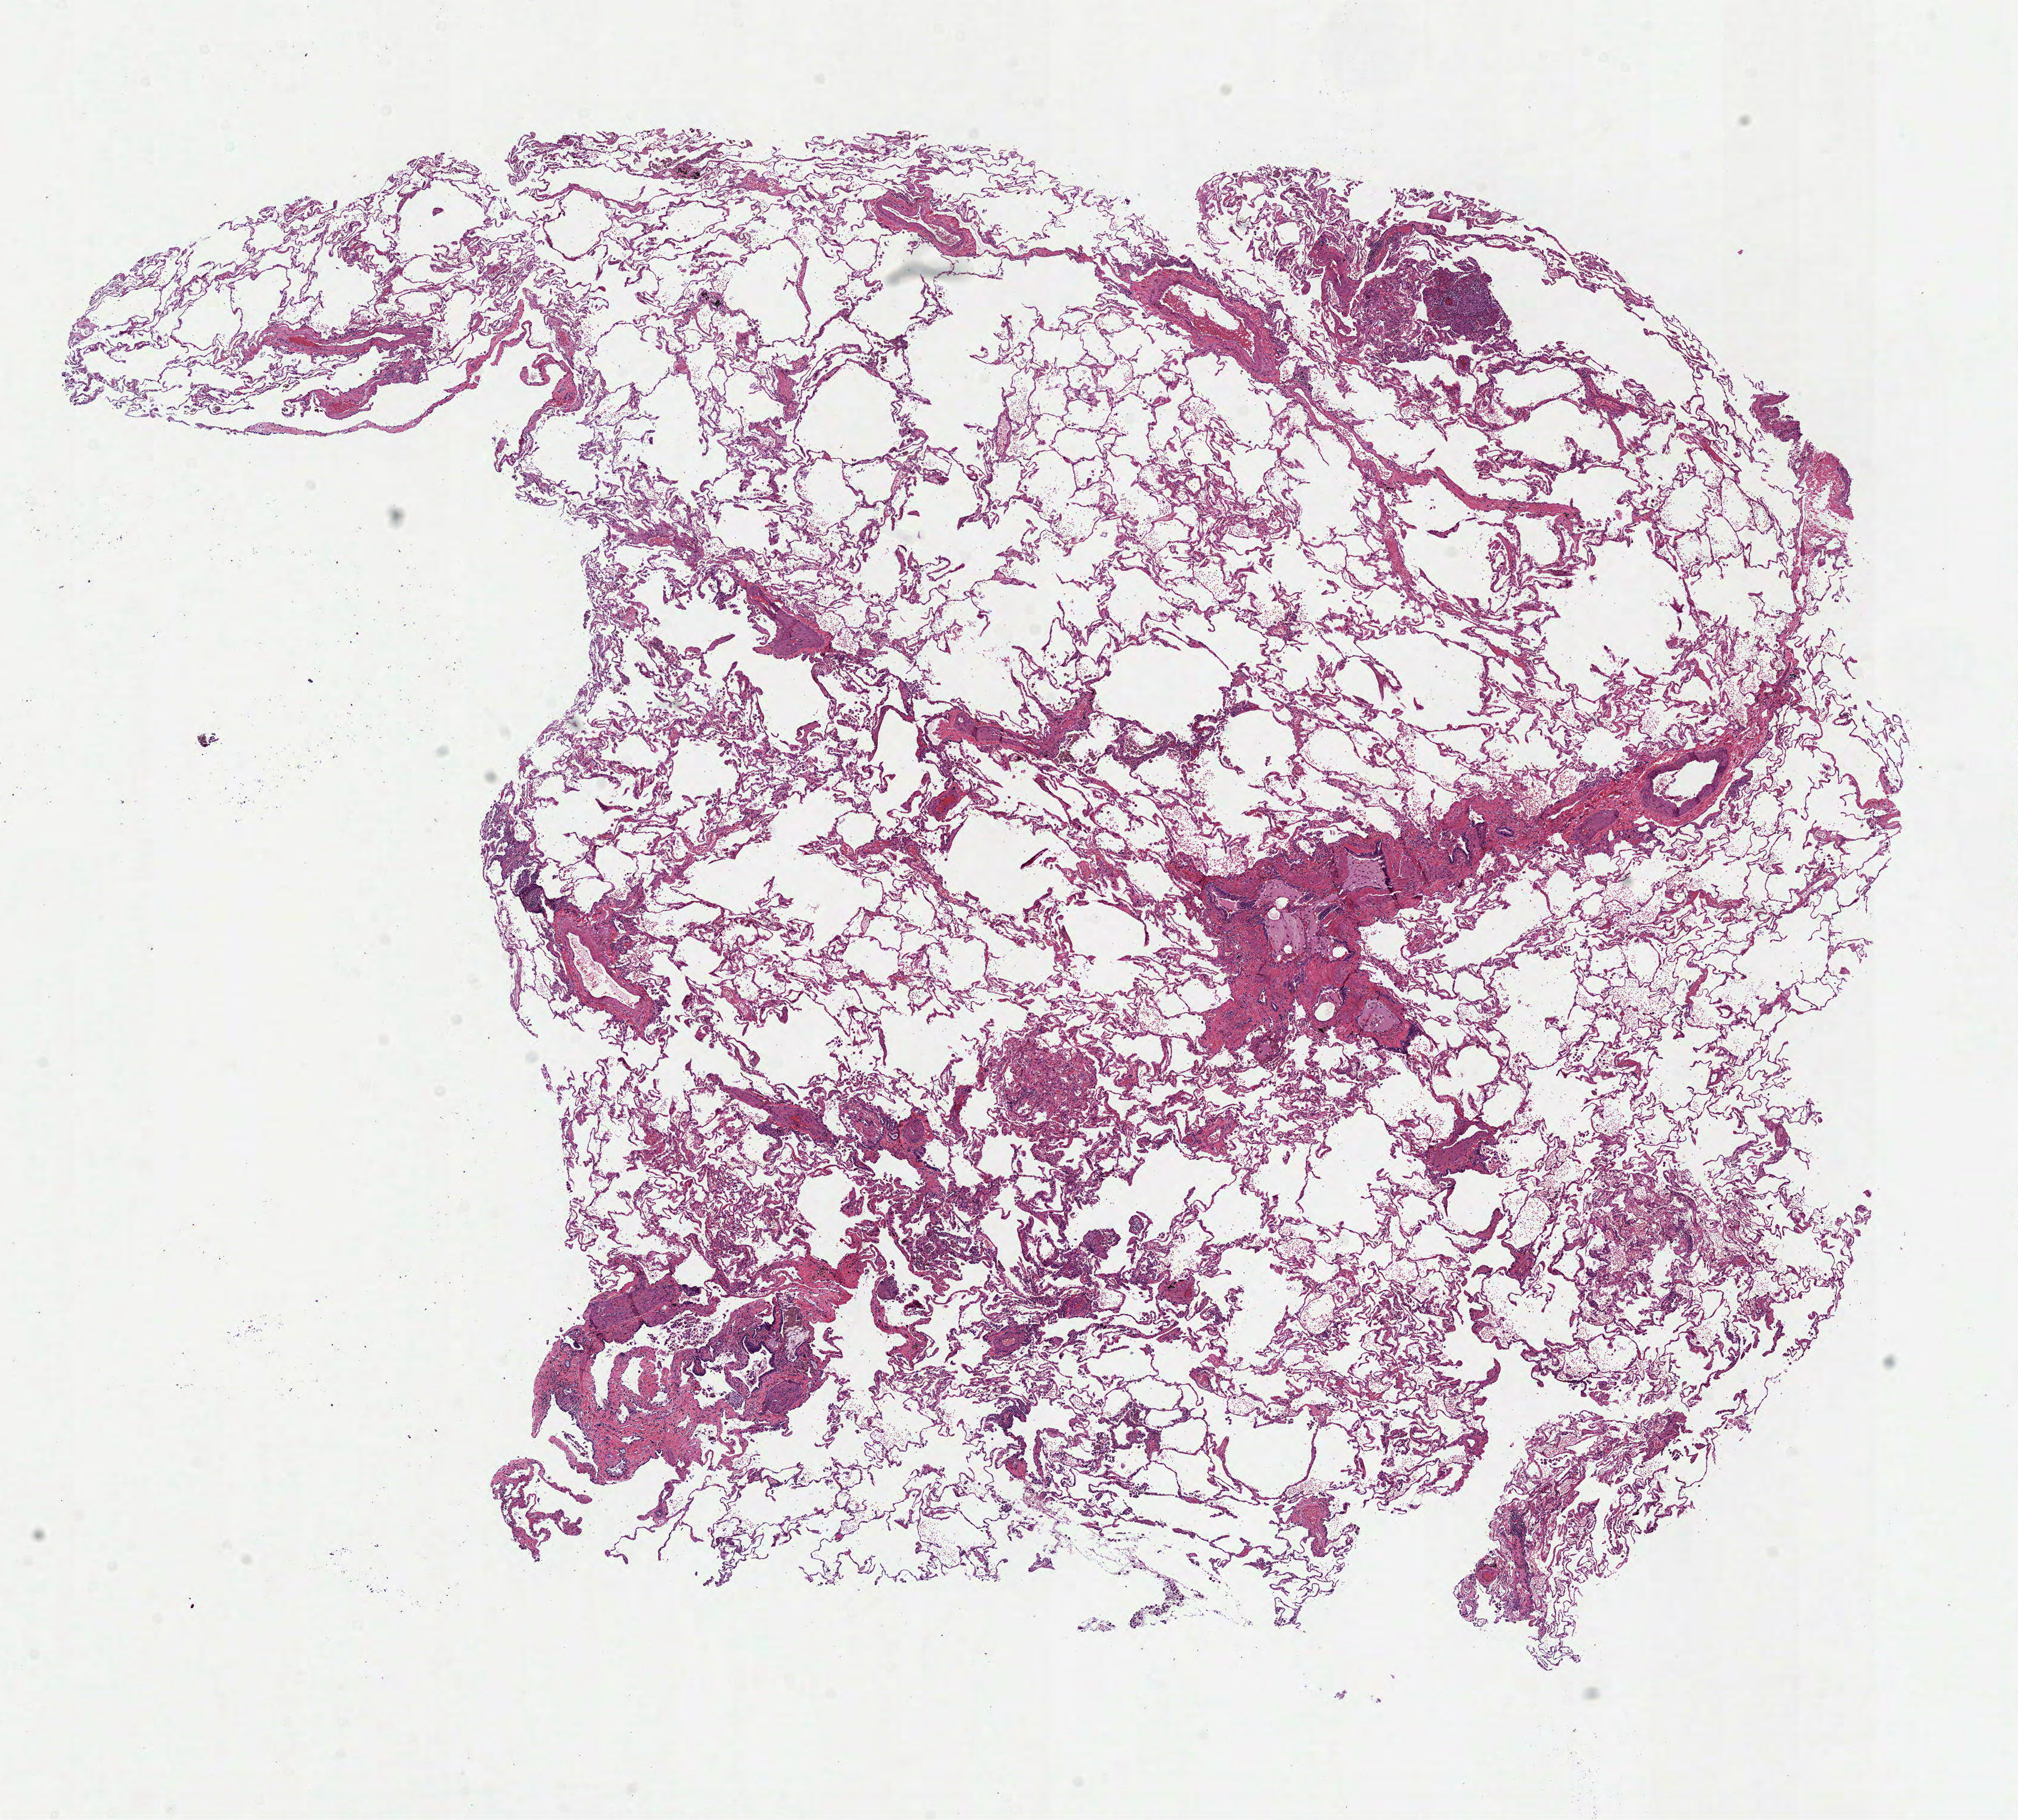
H&E-stained whole-slide image, low-resolution overview of the scanned area, about 13.6 x 12.2 mm (acquisition: 40x scan). Frozen section from the top of the tissue portion. Lung, solid tissue normal (non-tumour tissue) sample. Male patient; age at initial diagnosis 58 years.
* this section: solid tissue normal (non-tumour) sample from the same patient
* patient diagnosis: Adenocarcinoma, NOS (upper lobe, lung)